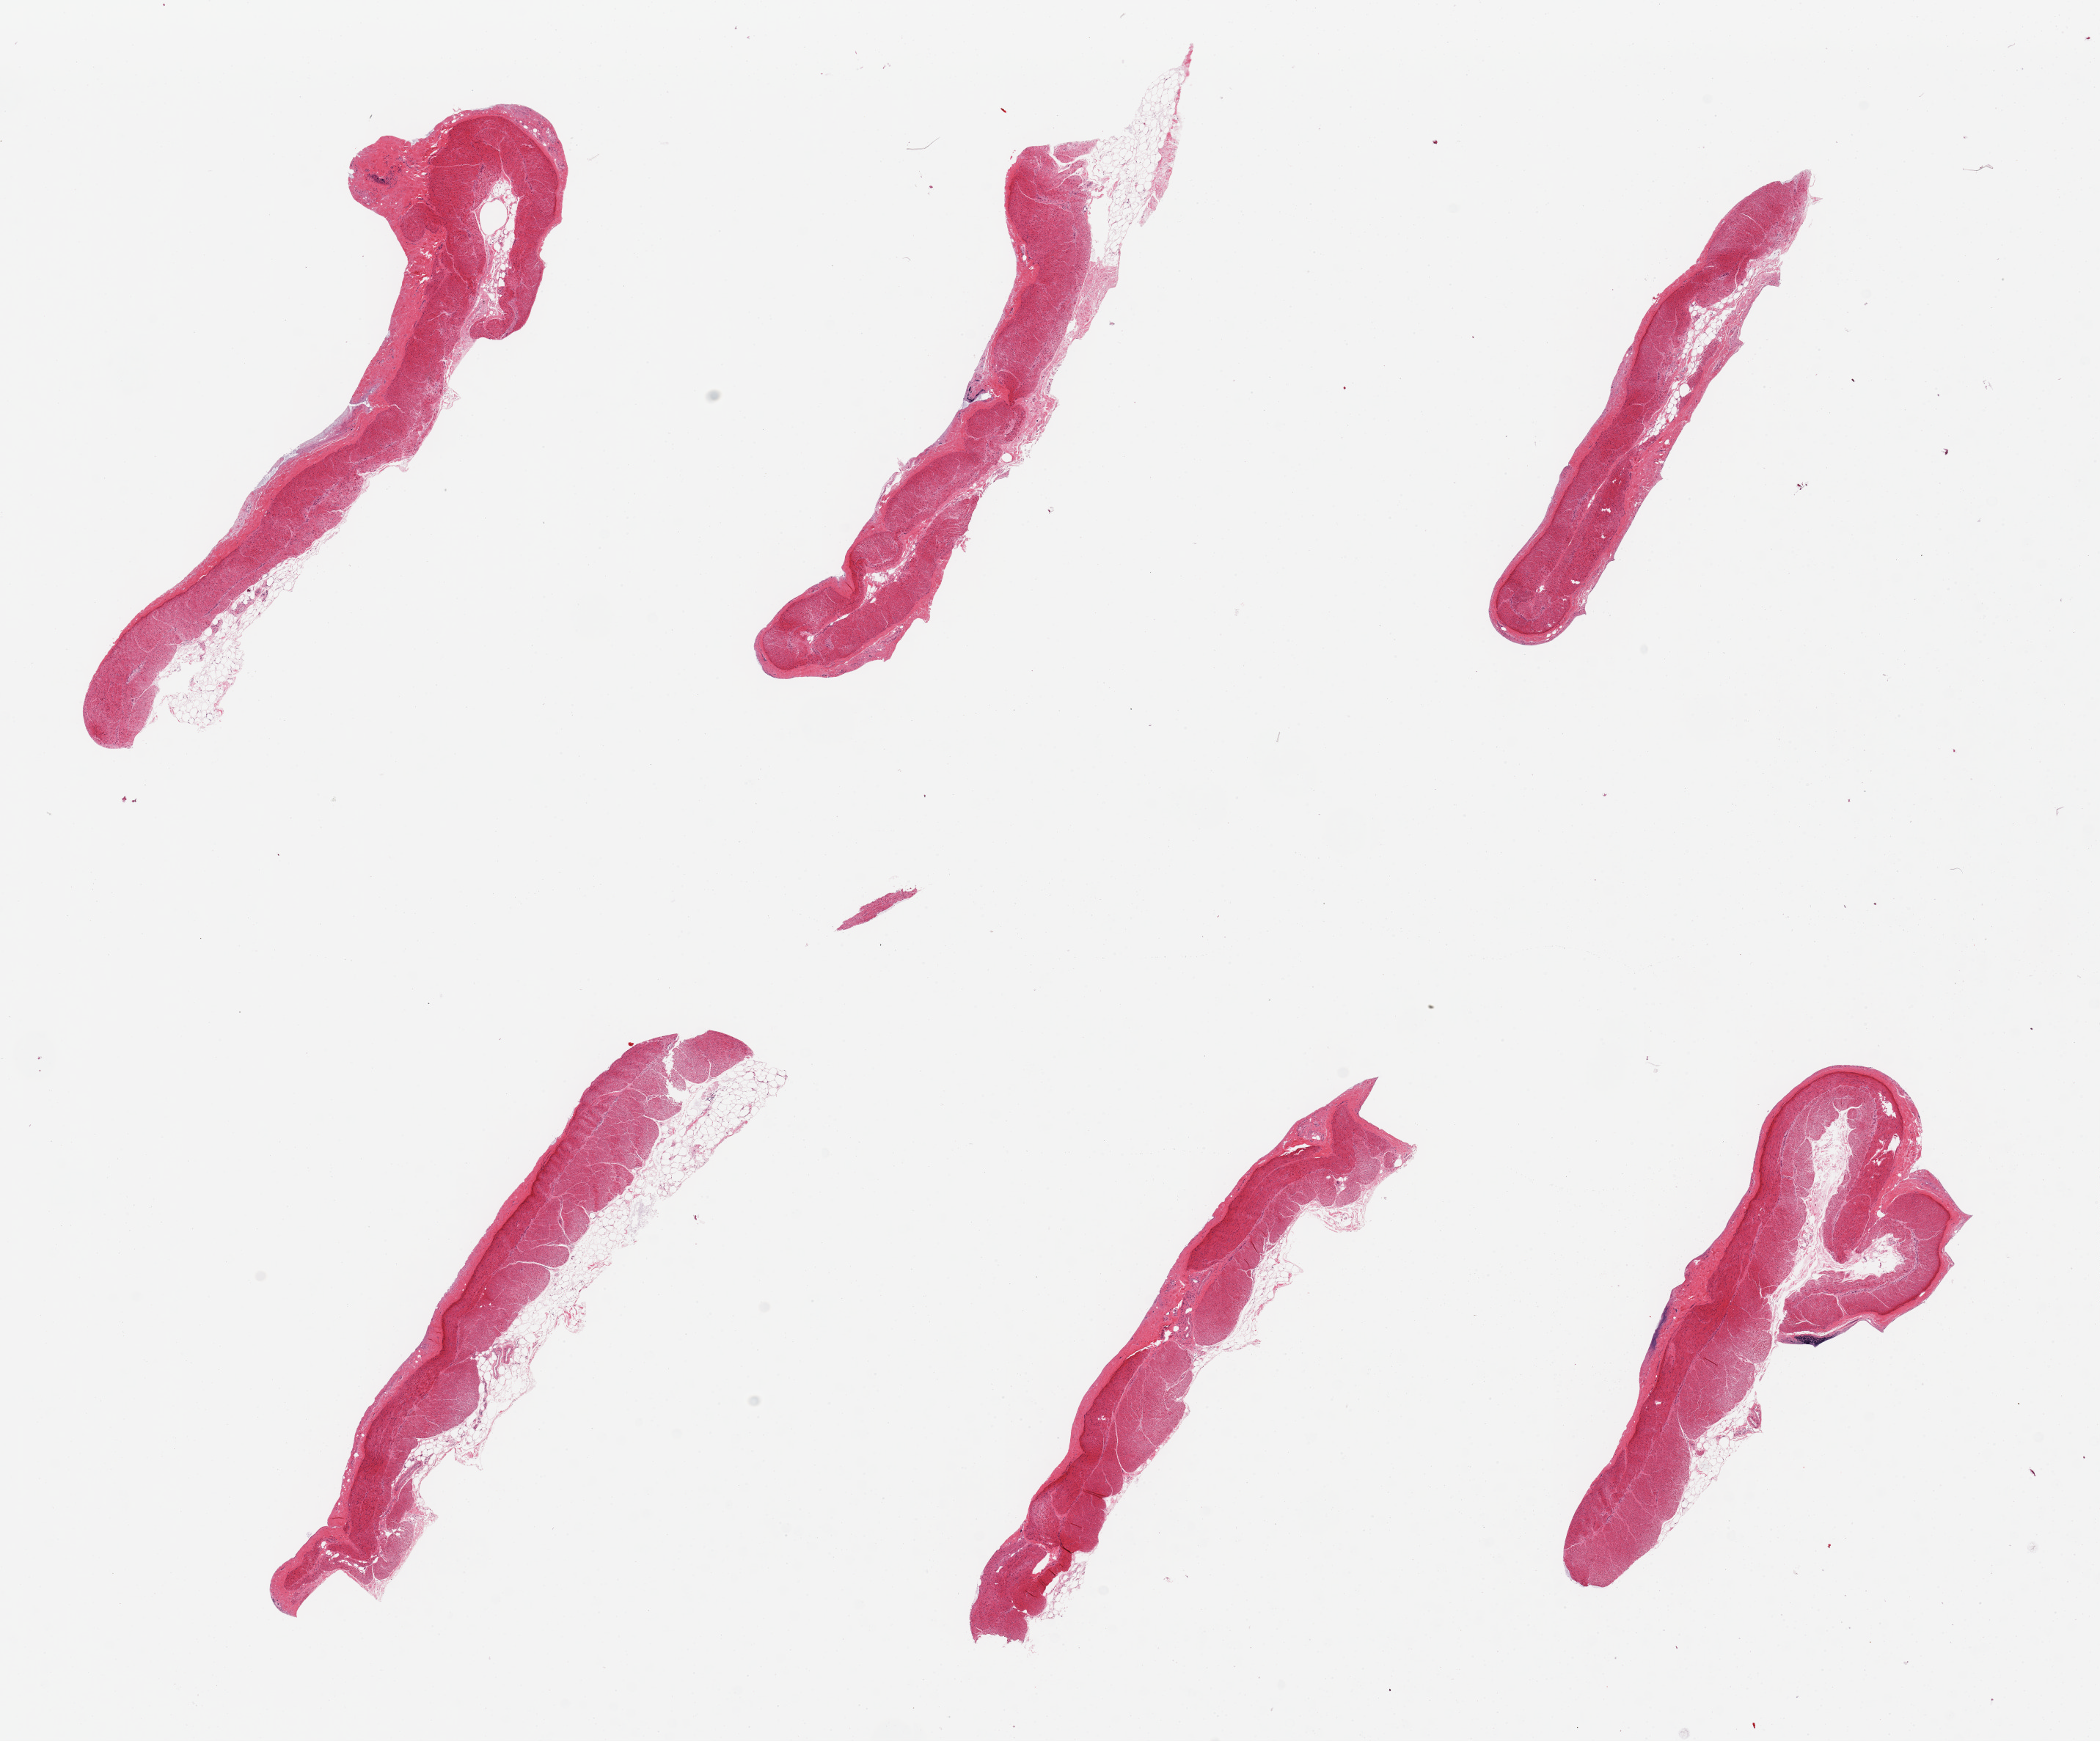
Digitized H&E-stained section — whole scanned area (about 22.6 x 18.8 mm, slide scanned at 20x) shown as a low-resolution overview. PAXgene-fixed paraffin-embedded (PFPE) section. Section of sigmoid colon (target tissue). Tissue donor sample. Donor sex: male.
- review note (as recorded): 6 pieces, all muscularis